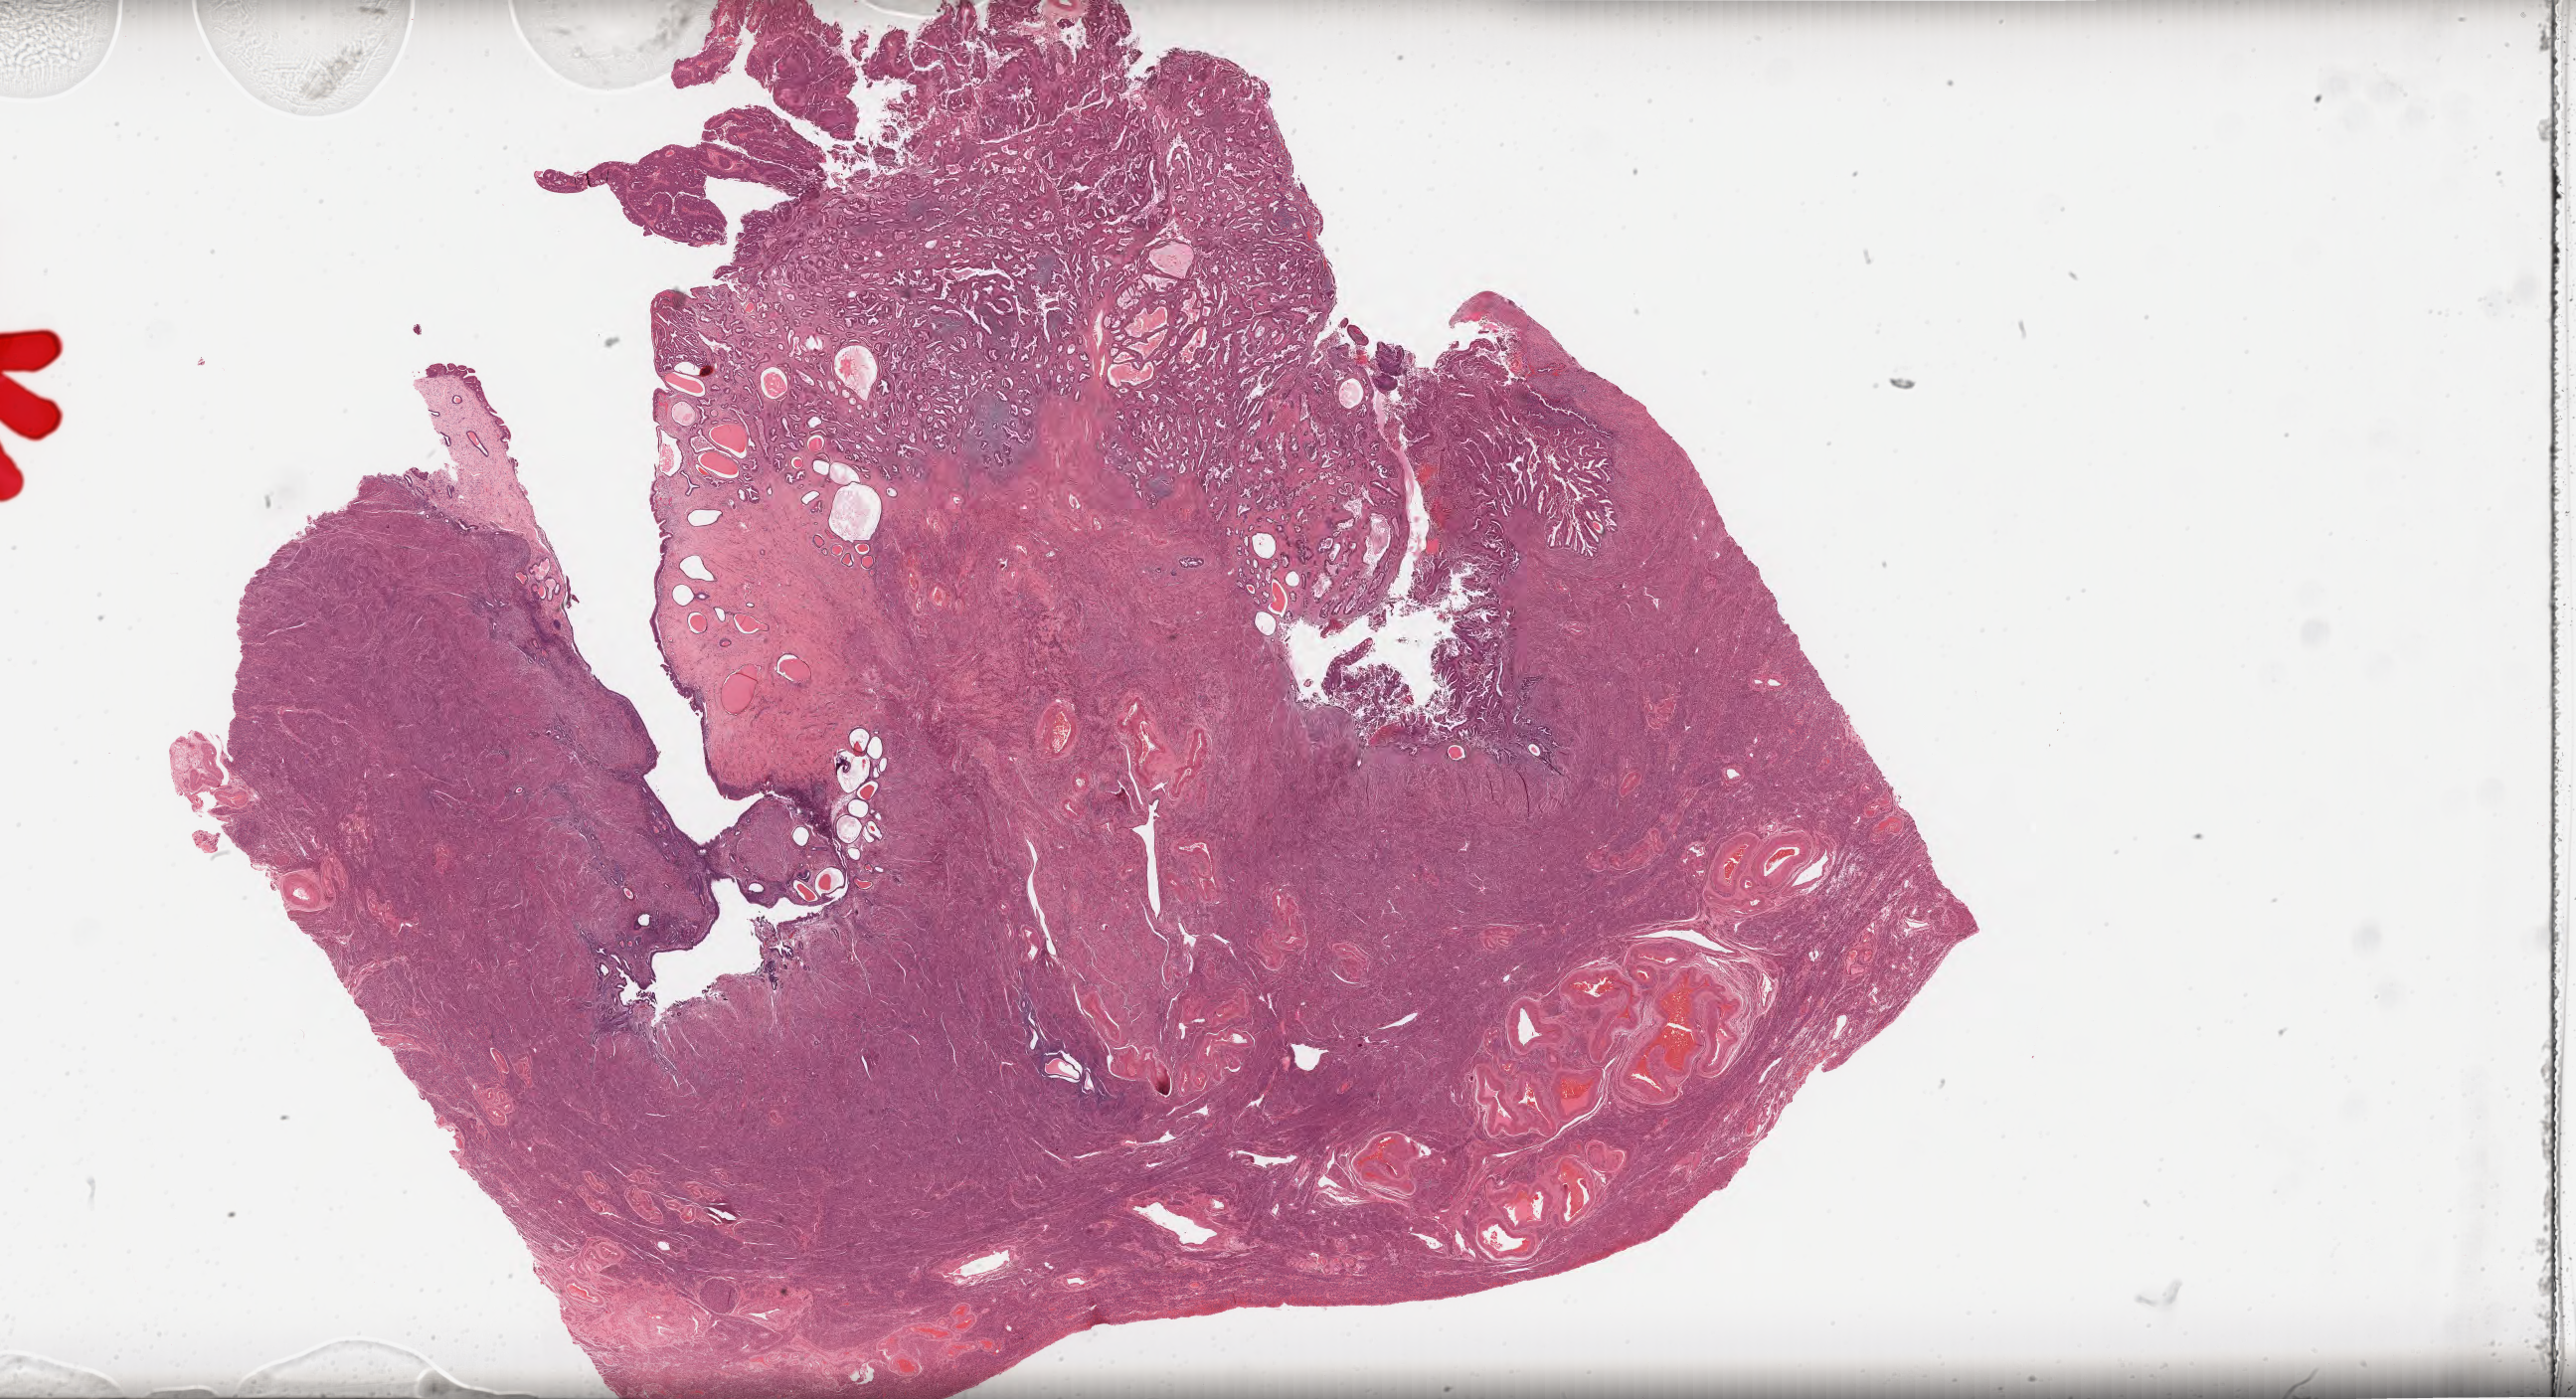
H&E-stained whole-slide image — a low-resolution overview of the entire scanned area, about 41.8 x 22.7 mm (slide scanned at 40x), formalin-fixed paraffin-embedded (FFPE) diagnostic section, sample: primary tumour, uterus. Female, age 72 years at initial diagnosis. Histologic grade: G3 (poorly differentiated).
• FIGO stage: IA
• histologic diagnosis: Serous cystadenocarcinoma, NOS